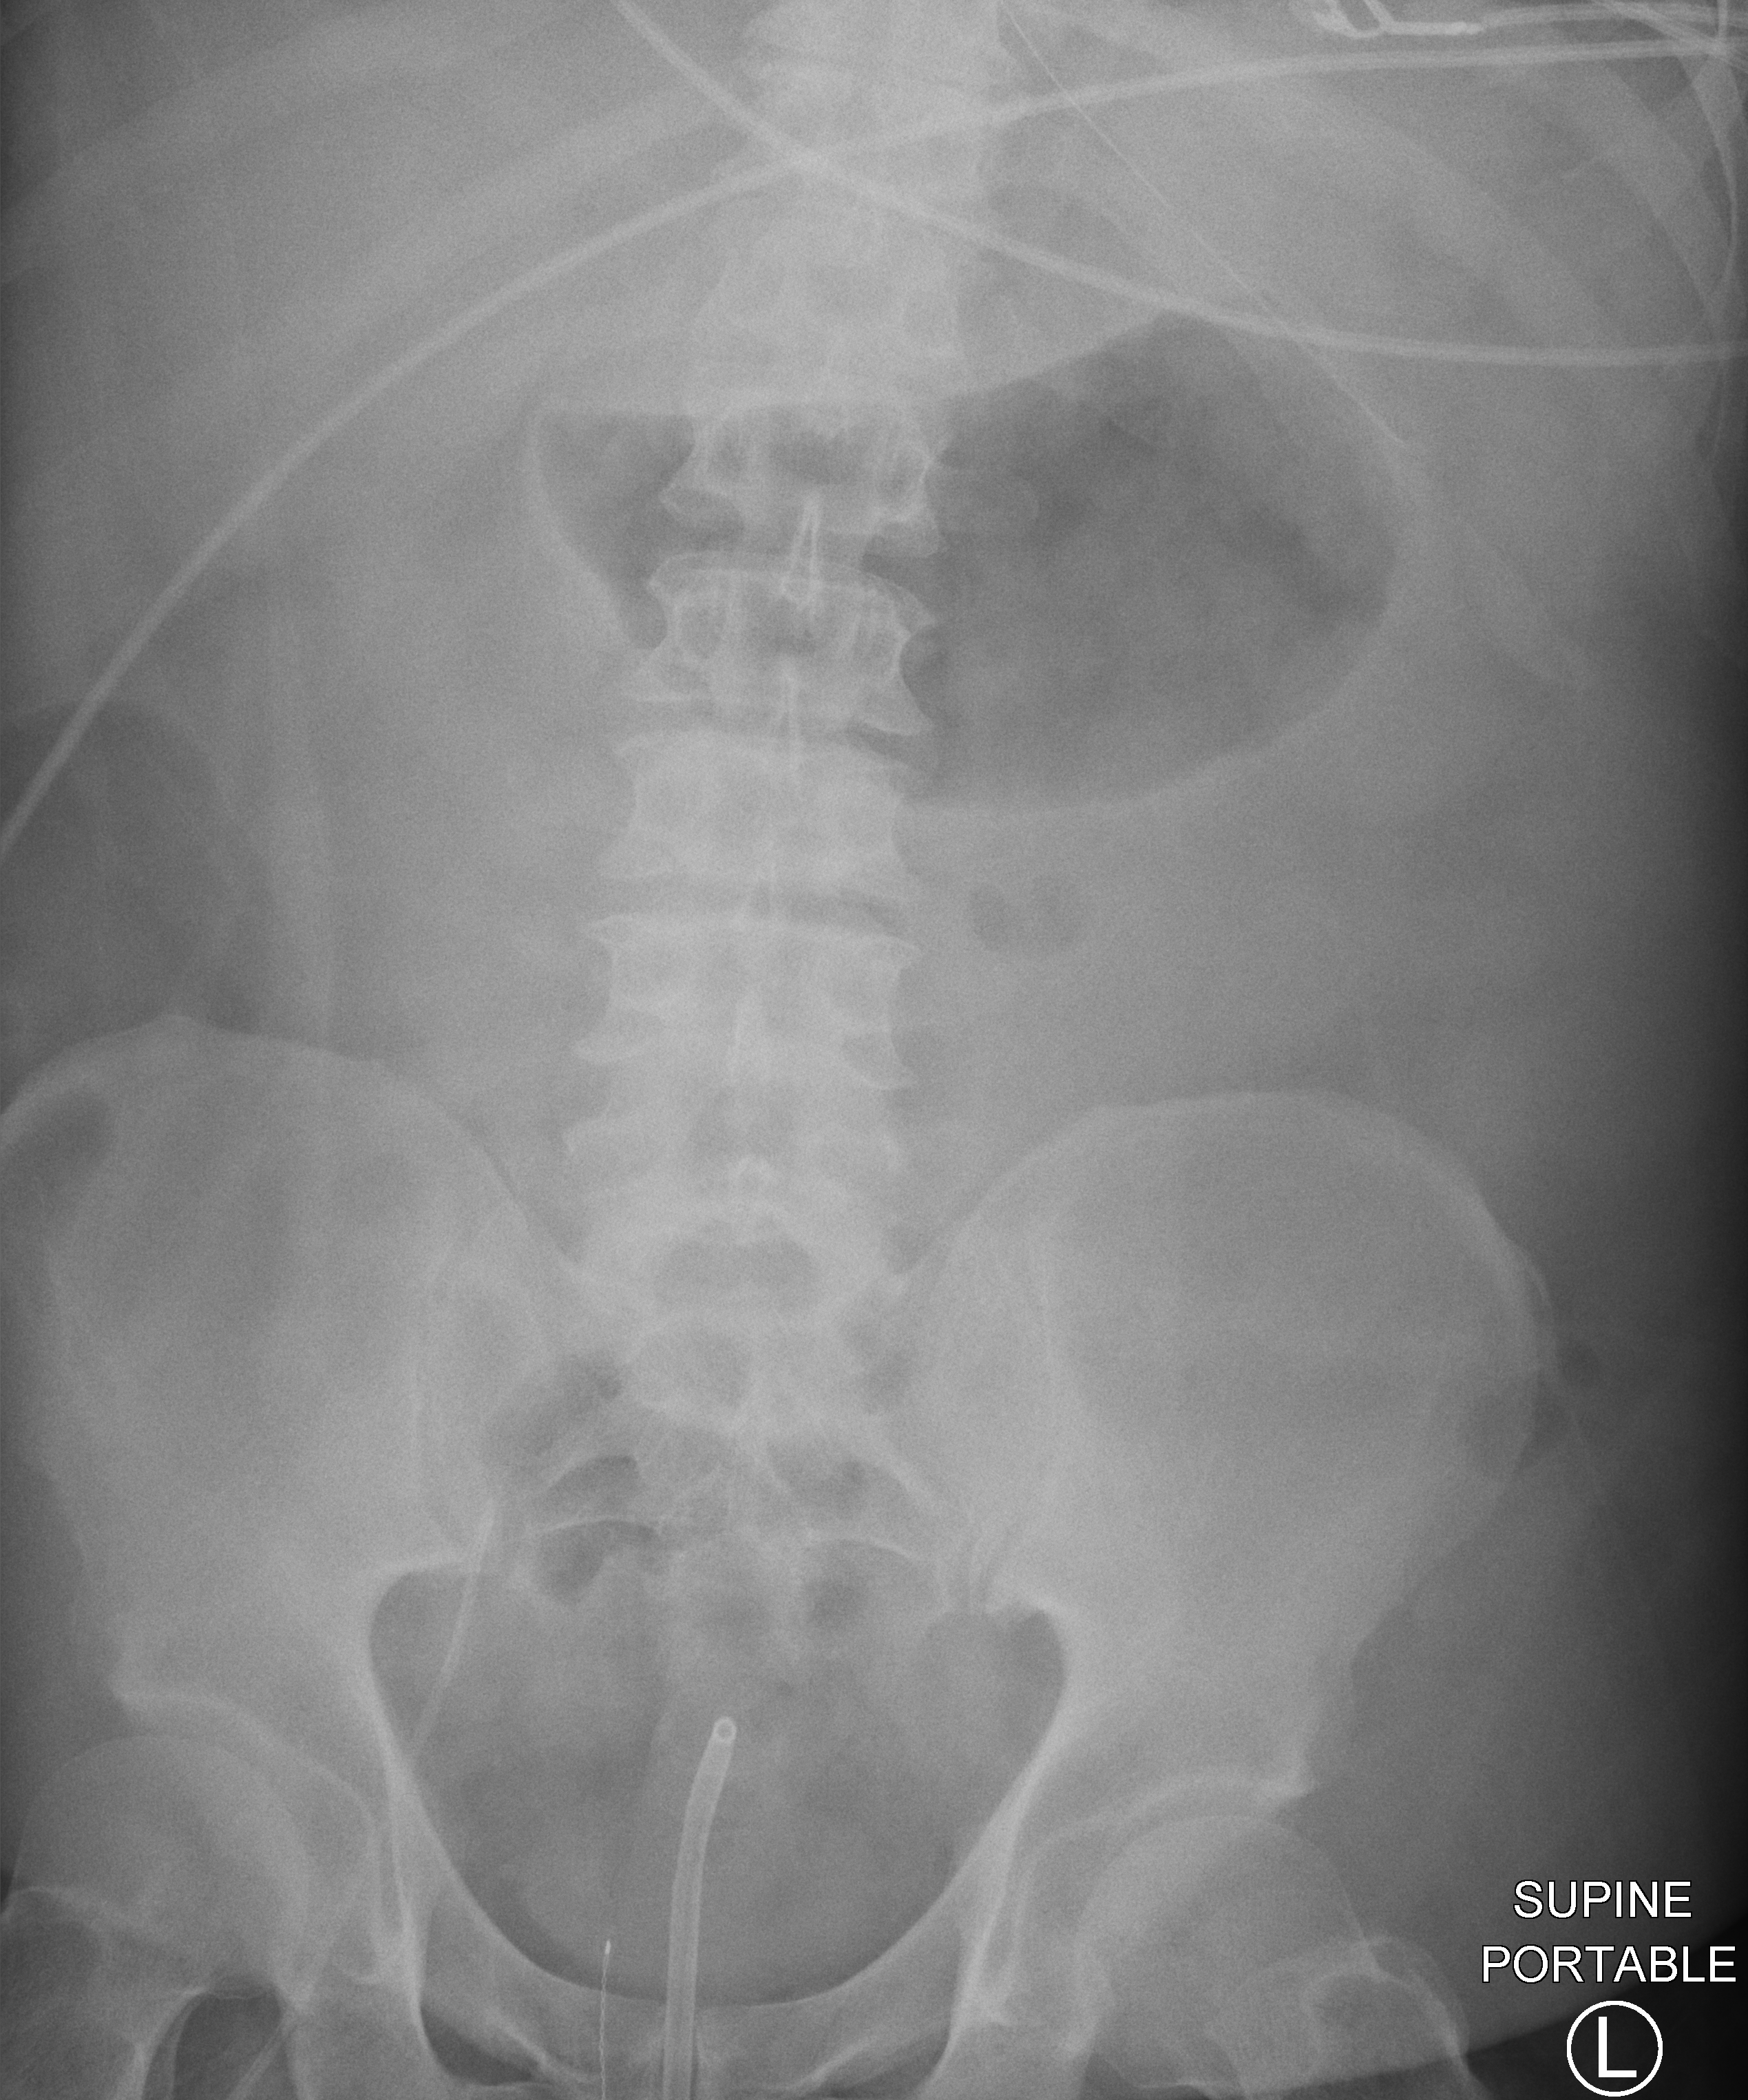
Bedside abdomen radiograph (computed radiography); anteroposterior (AP) projection. Male patient hospitalised with COVID-19, age 18–59 years.
Admission-level facts for this patient (not findings on this image; timing relative to this image not recorded):
- admitted to intensive care during this hospital stay: yes
- length of hospital stay: 28 days